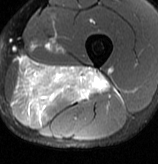
MRI of an extremity soft-tissue mass, one axial slice. Position 34 of 70 along the scan axis. T2-weighted fat-saturated. MR volume resampled by the dataset authors to the PET/CT grid (not the native acquisition matrix). 3.27 mm slice thickness. 158 × 164 image matrix, field of view 154 × 160 mm. Male patient. From the clinical record (not read from this slice): histological type: extraskeletal osteosarcoma; grade: high; site of the primary tumour: left adductur.
Annotated regions visible in this slice (expert contour drawn on MRI and transferred to this co-registered scan by the dataset authors):
- gross tumour volume (mass): bounding box <11,57,112,125> (left, top, right, bottom; pixels)